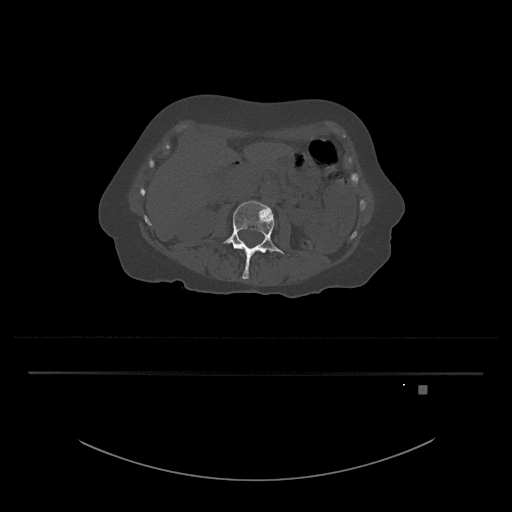
CT including the spine, one axial slice; position 430 of 797 along the scan axis; 120 kVp; bone window (W 1800 / L 400 HU); 512 × 512 image matrix, field of view 500 × 500 mm. Female patient, age 57 years. Case-level facts recorded for this patient, not image findings: primary cancer: cervical.
Outlined on this slice (semi-automatically segmented with operator editing):
- L3 vertebra: bounding box (x1, y1, x2, y2) in pixels: (223, 201, 286, 279)